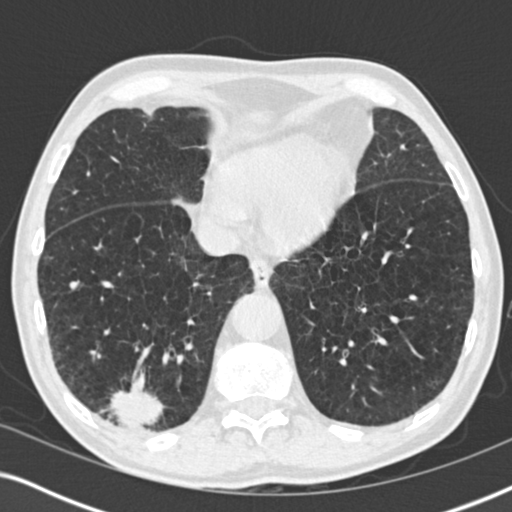
Low-dose screening chest CT, axial slice, first (baseline) screen, lung window (W 1500 / L -600 HU), standard (soft-tissue) reconstruction kernel (B30f). Male participant, aged 64 years at enrolment. Former smoker at enrolment.
Lesion marked by an expert reader, box from (x=85, y=370) to (x=179, y=448) px. The screening reader recorded 3 non-calcified nodules or masses ≥4 mm on this exam (lingula, lingula, right lower lobe); which of them this box marks is not recorded. Official screen result: positive, change unspecified: nodule(s) >= 4 mm or enlarging nodule(s), mass(es), or other non-specific abnormalities suspicious for lung cancer. Participant outcome: lung cancer diagnosed 27 days after this screen — squamous cell carcinoma, NOS, right lower lobe, moderately differentiated (G2), stage IV (AJCC 6th edition), 40 mm at pathology.